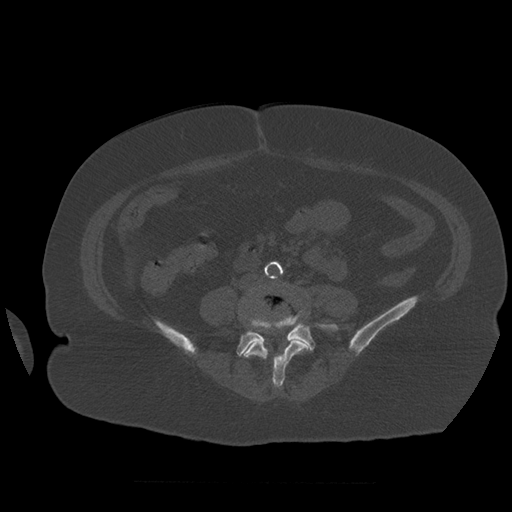
CT including the spine, one axial slice; position 194 of 399 along the scan axis; reconstruction kernel STANDARD; 120 kVp; bone window (W 1800 / L 400 HU); 1.25 mm slice thickness; 512 × 512 image matrix, field of view 404 × 404 mm. Patient age 81 years. From the clinical record (not read from this slice): primary cancer: renal; vertebrae with lytic lesions (as recorded): L1.
Annotated regions visible in this slice (semi-automatically segmented with operator editing):
- L4 vertebra: bounding box (x1, y1, x2, y2) in pixels: (244, 316, 310, 388)
- L5 vertebra: (237, 311, 338, 357)